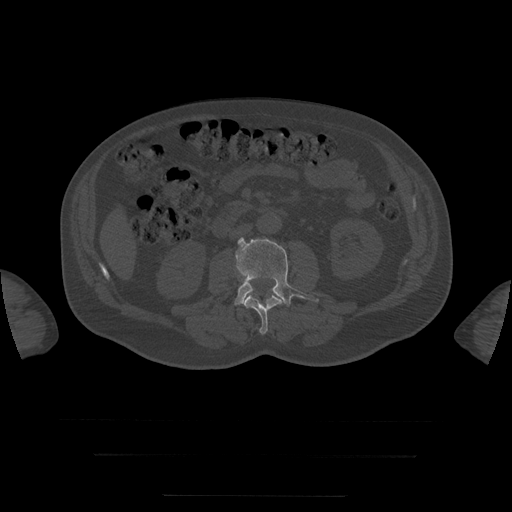
CT including the spine, one axial slice; position 7 of 397 along the scan axis; reconstruction kernel STANDARD; 120 kVp; bone window (W 1800 / L 400 HU); 1.25 mm slice thickness; 512 × 512 image matrix. Patient age 73 years. From the clinical record (not read from this slice): primary cancer: prostate.
Annotated regions visible in this slice (semi-automatic segmentation, software-assisted and operator-edited):
- L3 vertebra: box from (x=235, y=238) to (x=319, y=307) px